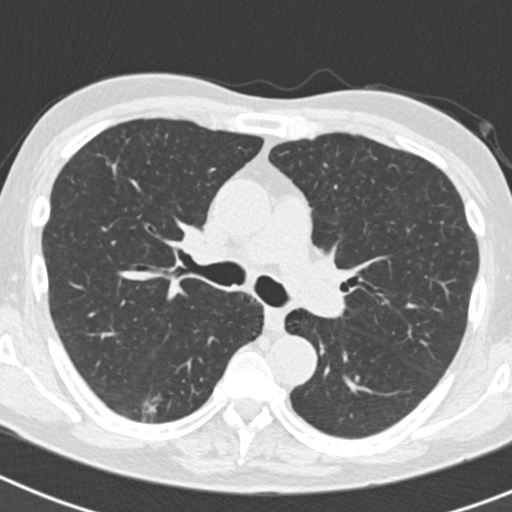
Low-dose screening chest CT, axial slice; second annual screen; lung window (W 1500 / L -600 HU); 2 mm slice thickness; 120 kVp; 512 × 512 image matrix, field of view 300 × 300 mm. Male participant, aged 70 years at enrolment. Current smoker at enrolment.
Expert-annotated lung lesion, bounding box (x1, y1, x2, y2) in pixels: (136, 383, 193, 435). The screening reader recorded 5 non-calcified nodules or masses ≥4 mm on this exam; which of them this box marks is not recorded. Participant outcome: lung cancer diagnosed 622 days after this screen (after the third annual screen) — bronchiolo-alveolar adenocarcinoma, NOS, right lower lobe, poorly differentiated (G3), stage IB (AJCC 6th edition), 30 mm at pathology.